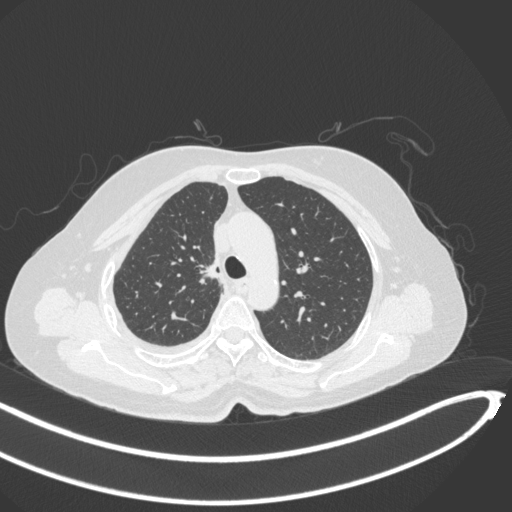
Chest CT, one axial slice. Position 222 of 297 along the scan axis. Reconstruction kernel B31f. 120 kVp. Lung window (W 1500 / L -600 HU). 512 × 512 image matrix, field of view 400 × 400 mm. Patient: female, 64 years. Case-level facts recorded for this patient, not image findings: clinical TNM (as recorded): T1b N0 M1.
Structures marked on this image (rectangle marked by the reading radiologist):
- lung tumour (recorded histology: adenocarcinoma): bounding box (x1, y1, x2, y2) in pixels: (200, 256, 220, 285)